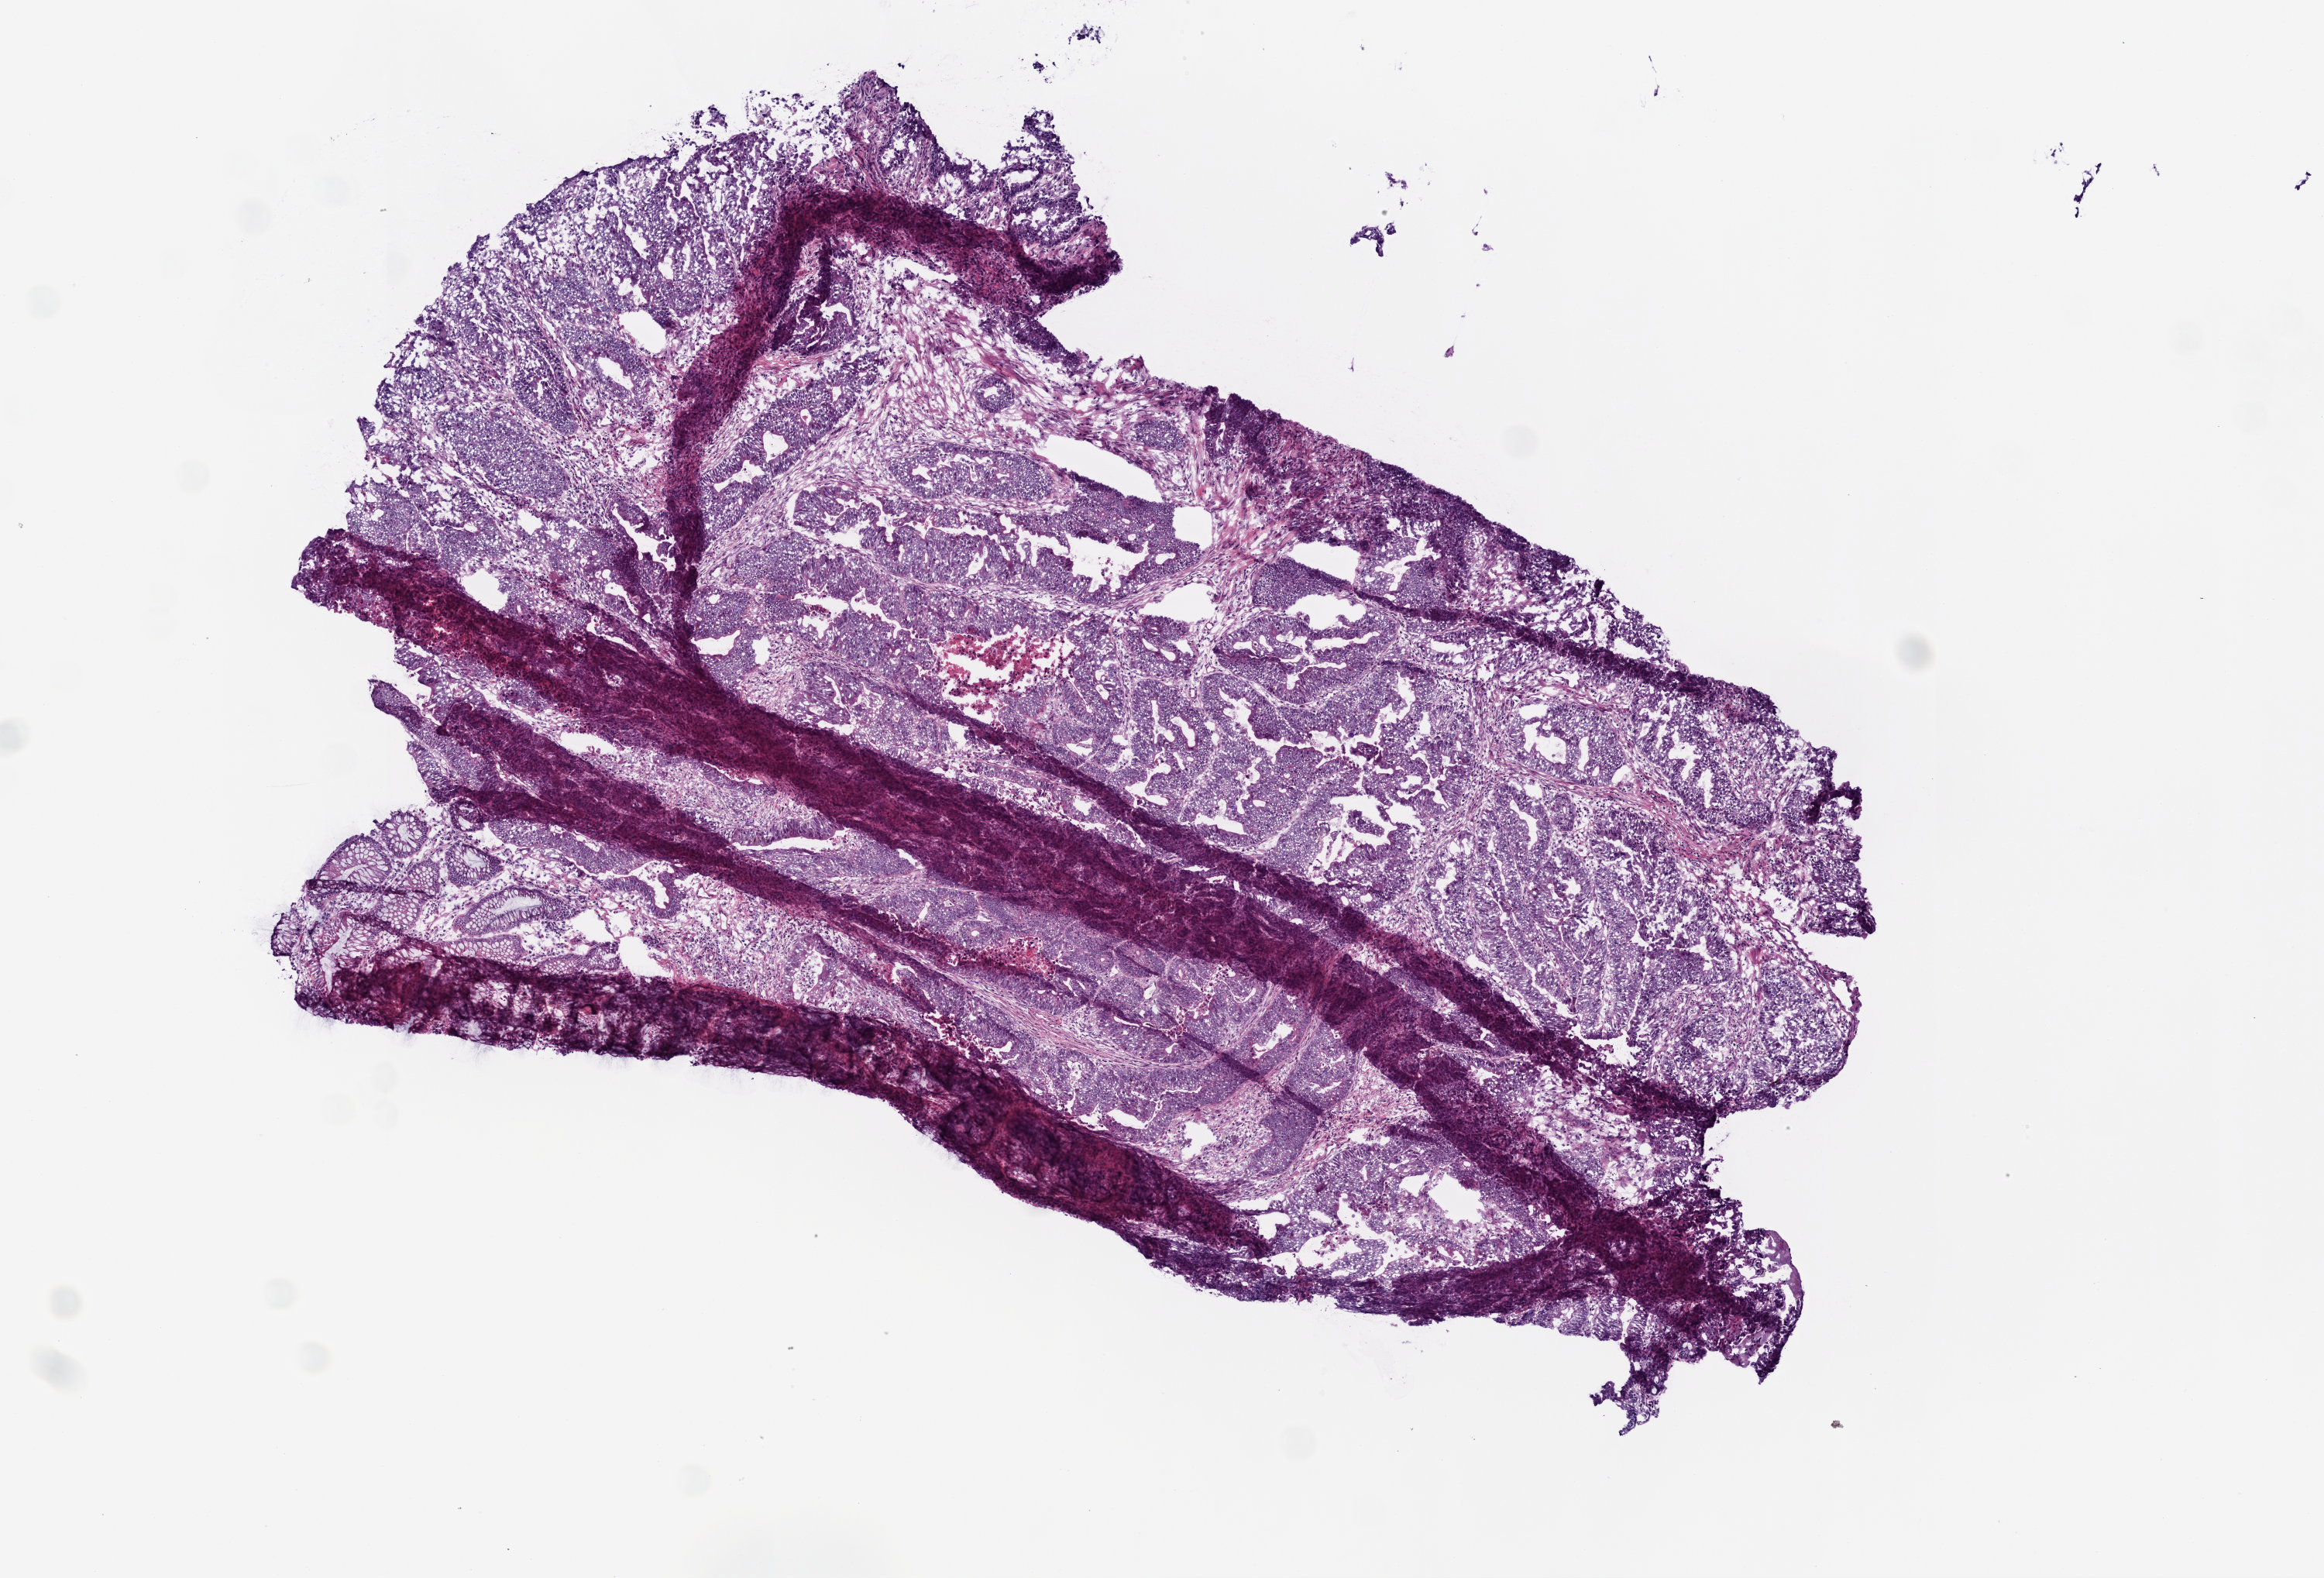
Whole-slide histology image, Hematoxylin and eosin (H&E) stained — low-resolution overview of the scanned area, about 6.0 x 4.1 mm (acquisition: 20x scan). Frozen section from the top of the tissue portion. Primary tumour sample from the colon. Male, age 79 years at initial diagnosis. Composition of this section per pathologist review: tumour cells 85%, tumour nuclei 75%, normal cells 0%, stromal cells 10%, necrosis 5%.
- diagnosis: Adenocarcinoma, NOS (ascending colon)
- AJCC pathologic stage: I (5th edition)
- TNM: T2 N0 M0